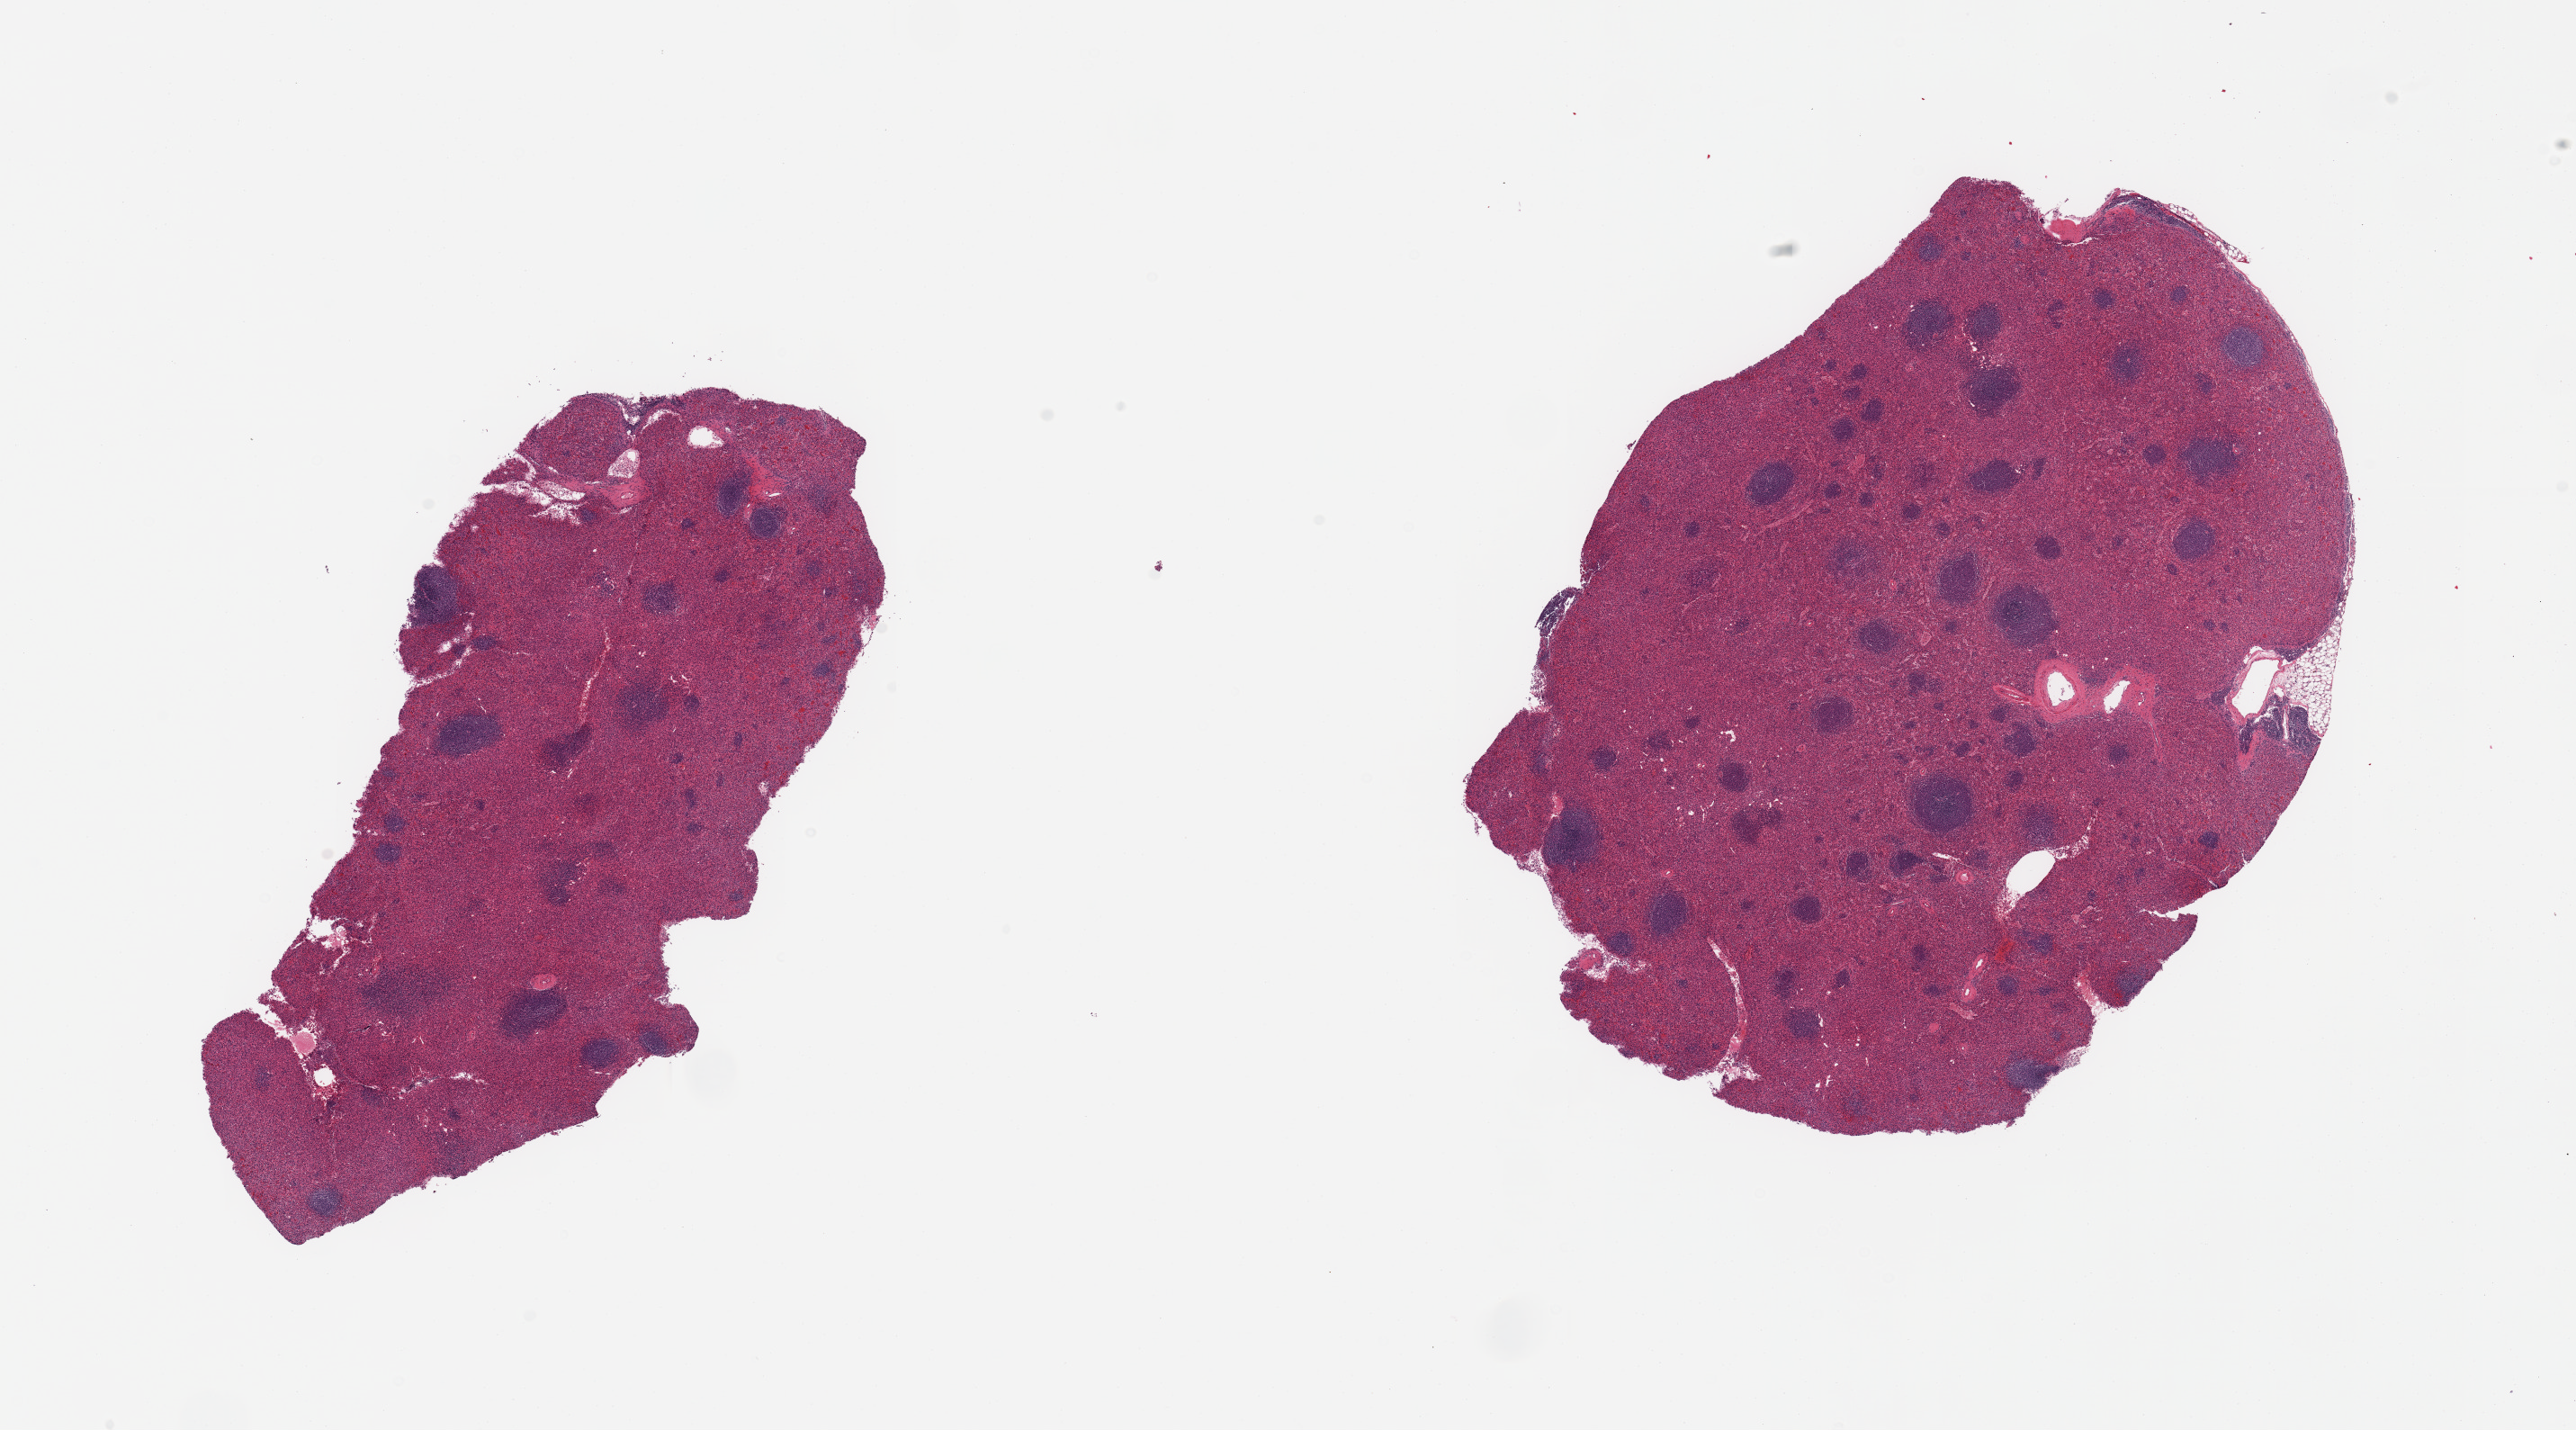
Digitized hematoxylin and eosin (H&E)-stained section — shown as a low-resolution overview of the whole scanned area (about 22.6 x 12.6 mm); PAXgene-fixed, paraffin-embedded tissue; section of adrenal gland (target tissue); donor tissue sample. Donor sex: male.
- reviewer comment on this tissue sample: 2 pieces; spleen, not adrenal